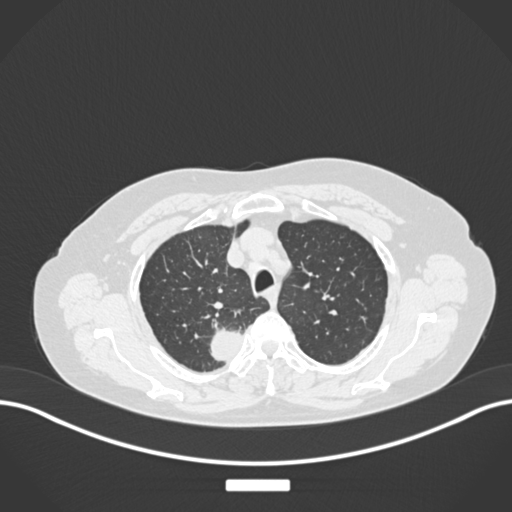
Chest CT, one axial slice; position 207 of 237 along the scan axis; reconstruction kernel B30f; lung window (W 1500 / L -600 HU); 1 mm slice thickness; 512 × 512 image matrix, field of view 400 × 400 mm. Patient: female, 62 years. From the clinical record (not read from this slice): clinical TNM (as recorded): T1c N1 M0.
Structures marked on this image (bounding box drawn by a radiologist):
- lung tumour (recorded histology: squamous cell carcinoma): bounding box (x1, y1, x2, y2) in pixels: (205, 325, 246, 366)